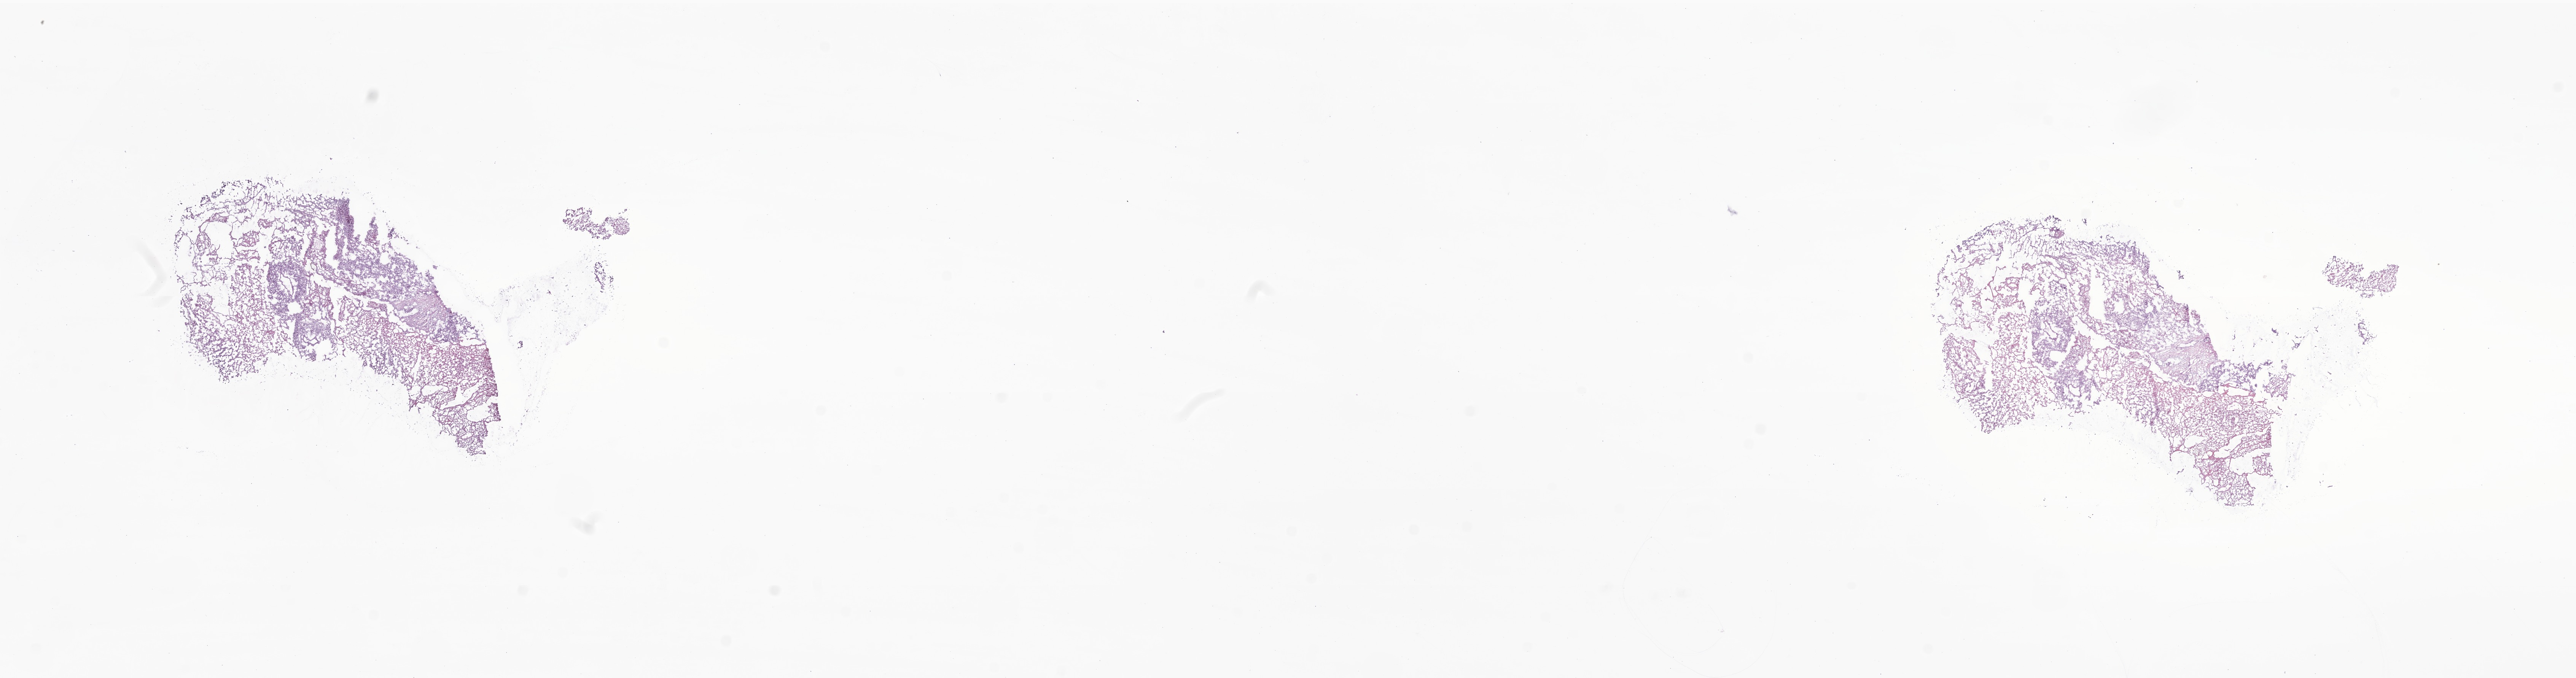
Digitized hematoxylin and eosin (H&E)-stained section of tumor tissue from the adrenal gland, a low-resolution overview of the entire scanned area, about 28.5 x 7.5 mm; frozen section. Patient: female, age 621 days (about 1.7 years).
• recorded diagnosis: Neuroblastoma, NOS